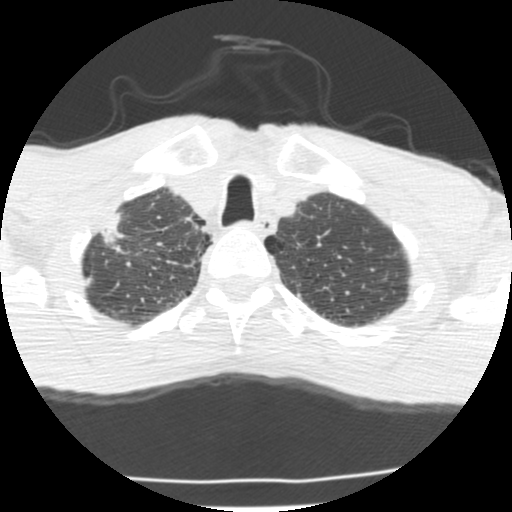
Low-dose screening chest CT, one axial slice; slice 186 of 214 in the series (ordered by position); 120 kVp; lung window (W 1500 / L -600 HU); 2.5 mm slice thickness; 512 × 512 image matrix, field of view 283 × 283 mm.
Structures marked on this image (expert manual segmentation):
- lesion 1 (tumor, upper lobe of right lung): bounding box <100,212,123,247> (left, top, right, bottom; pixels)